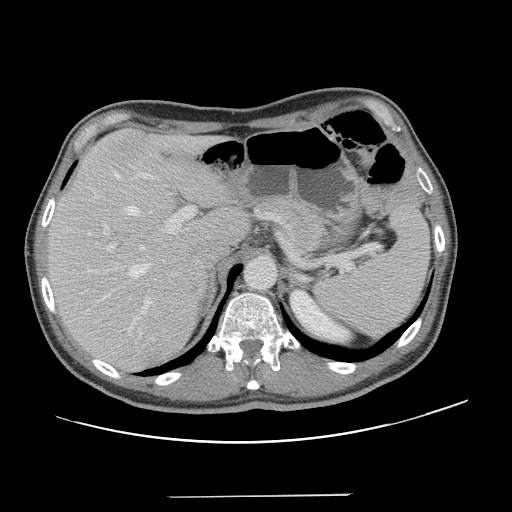
Contrast-enhanced abdominal CT, one axial slice; slice 92 of 131 in the series (ordered by position); 120 kVp; intravenous contrast given; soft-tissue window (W 400 / L 40 HU); 512 × 512 image matrix, field of view 403 × 403 mm. Male patient, age 60 years. Case-level facts recorded for this patient, not image findings: diagnosis: colorectal cancer liver metastases, imaged before liver resection; multiple liver metastases: no; largest metastasis: 2.5 cm; chemotherapy before resection: no.
Outlined on this slice (expert manual segmentation):
- hepatic veins: bounding box [x1, y1, x2, y2] px = [87, 171, 151, 311]
- liver: [47, 129, 247, 371]
- planned liver remnant (the part of the liver to remain after resection): [47, 129, 247, 354]
- portal vein (with intrahepatic branches): [102, 144, 196, 329]
- liver metastasis: [189, 285, 201, 296]